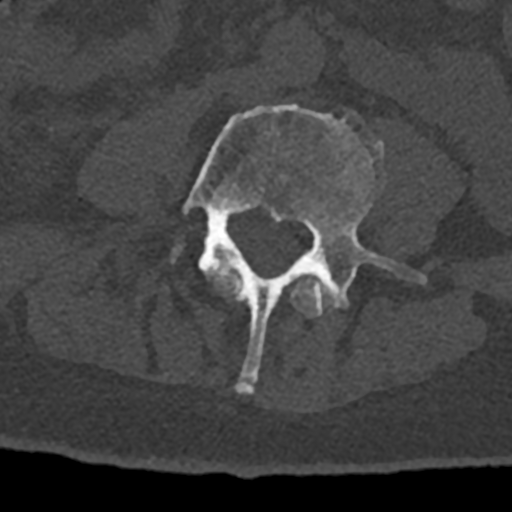
CT including the spine, one axial slice; slice 265 of 797 in the series (ordered by position); reconstruction kernel Br40s/3; 120 kVp; bone window (W 1800 / L 400 HU); 0.5 mm slice thickness; 512 × 512 image matrix, field of view 160 × 160 mm. Patient: male, 74 years. Case-level facts recorded for this patient, not image findings: primary cancer: renal.
Annotated regions visible in this slice (semi-automatically segmented with operator editing):
- L3 vertebra: bounding box (x1, y1, x2, y2) in pixels: (209, 267, 332, 317)
- L4 vertebra: (183, 104, 426, 393)
- L5 vertebra: (176, 249, 178, 253)